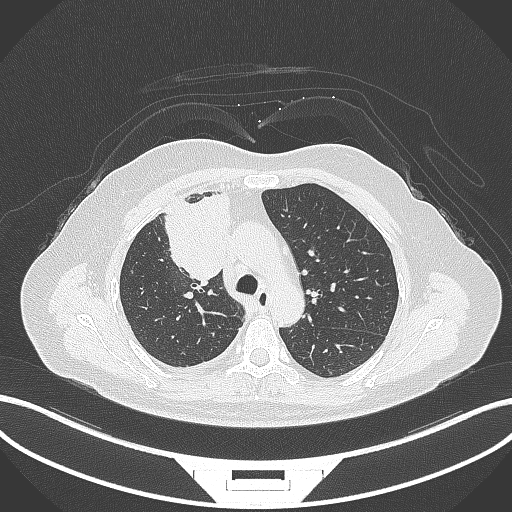
Chest CT, one axial slice; position 202 of 305 along the scan axis; 120 kVp; lung window (W 1500 / L -600 HU); 1 mm slice thickness; 512 × 512 image matrix, field of view 400 × 400 mm. Patient: female, 52 years. Case-level facts recorded for this patient, not image findings: clinical TNM (as recorded): T3 N1 M1.
Structures marked on this image (bounding box drawn by a radiologist):
- lung tumour (recorded histology: adenocarcinoma): bounding box [x1, y1, x2, y2] px = [157, 189, 234, 286]